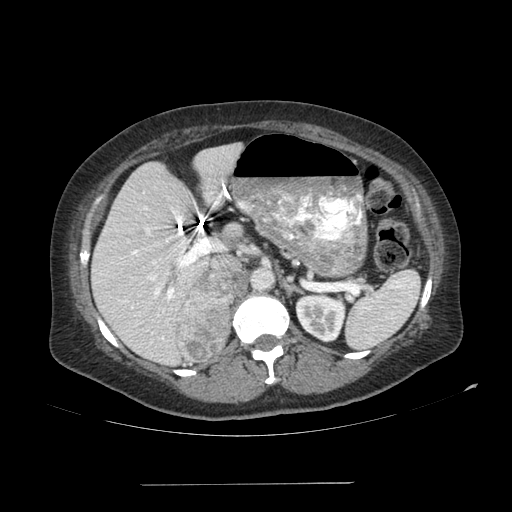
Contrast-enhanced abdominal CT, one axial slice; reconstruction kernel SOFT; soft-tissue window (W 400 / L 40 HU); 2.5 mm slice thickness; 512 × 512 image matrix, field of view 440 × 440 mm. Patient: female, 67 years. Case-level facts recorded for this patient, not image findings: diagnosis: adrenocortical carcinoma; tumour side: right adrenal; tumour size at pathology: 9.8 cm; Ki-67 index: 59 %; stage (as recorded): 4.
Outlined on this slice (semi-automatically segmented with operator editing):
- mass: bounding box (x1, y1, x2, y2) in pixels: (177, 272, 234, 361)